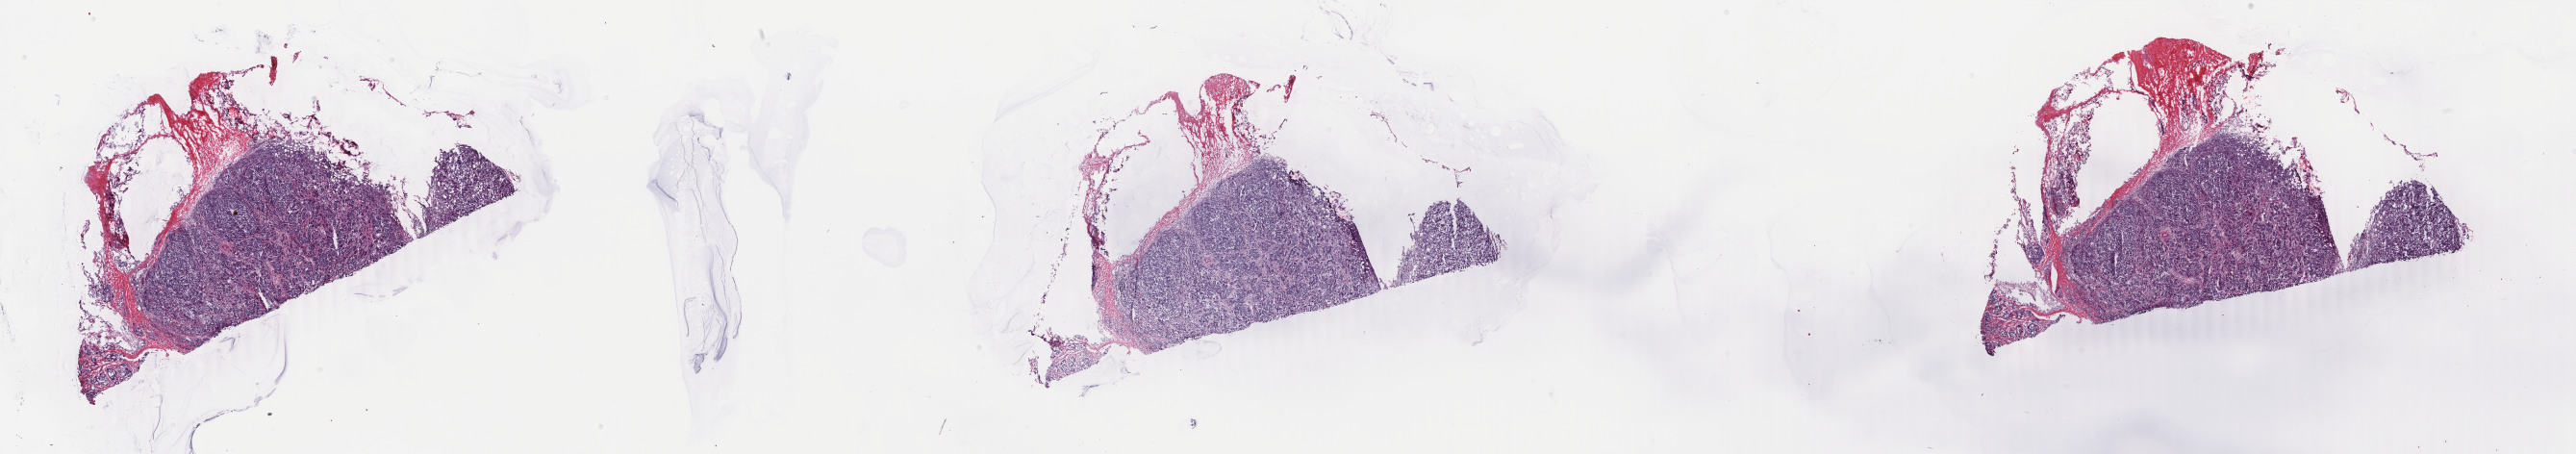
H&E-stained whole-slide image — a low-resolution overview of the entire scanned area, about 42.6 x 7.5 mm (slide scanned at 40x), frozen section, breast, primary tumour sample. Female, age 32 years at initial diagnosis. Pathologist review of this section (percent, as recorded): tumour cells 85%, tumour nuclei 90%, normal cells 0%, stromal cells 15%, necrosis 0%. Inflammatory infiltration, as recorded: lymphocyte infiltration 1%, monocyte infiltration 0%, neutrophil infiltration 0%.
• AJCC pathologic stage: IA
• lymph nodes positive (case pathology): 0 of 14 examined
• laterality: left
• TNM: T1b N0 M0
• histologic diagnosis: Infiltrating duct carcinoma, NOS